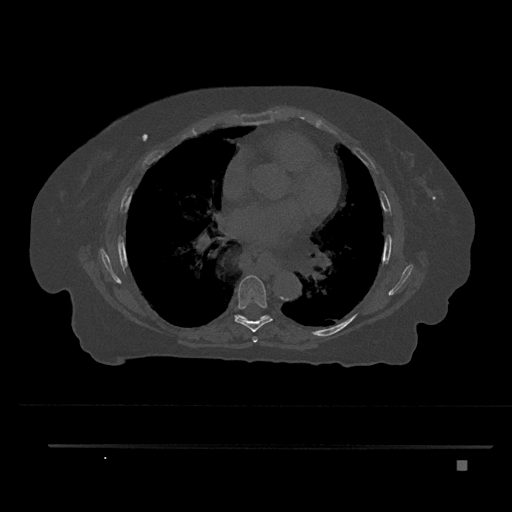
CT including the spine, one axial slice. Position 482 of 797 along the scan axis. Reconstruction kernel Br40s/3. Bone window (W 1800 / L 400 HU). 0.5 mm slice thickness. 512 × 512 image matrix, field of view 437 × 437 mm. Female patient, age 76 years. Case-level facts recorded for this patient, not image findings: primary cancer: lung; vertebrae with lytic lesions (as recorded): T11, L3.
Structures marked on this image (semi-automatically segmented with operator editing):
- T6 vertebra: bounding box [x1, y1, x2, y2] px = [252, 336, 258, 343]
- T7 vertebra: [234, 275, 273, 332]
- T8 vertebra: [236, 315, 270, 320]